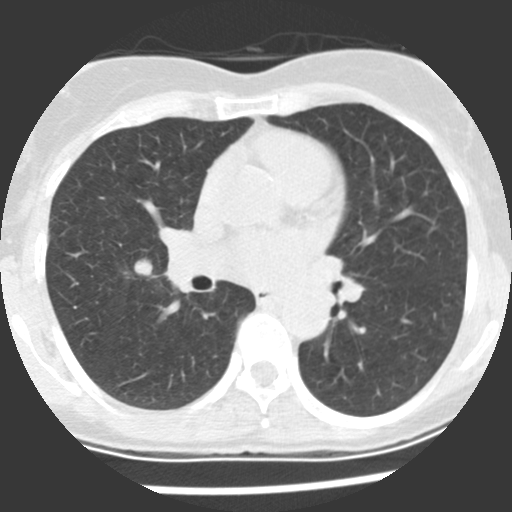
Low-dose screening chest CT, one axial slice; slice 118 of 225 in the series (ordered by position); reconstruction kernel STANDARD; 120 kVp; lung window (W 1500 / L -600 HU); 512 × 512 image matrix.
Annotated regions visible in this slice (expert manual segmentation):
- lesion 1 (tumor, upper lobe of right lung): bounding box <134,259,153,277> (left, top, right, bottom; pixels)